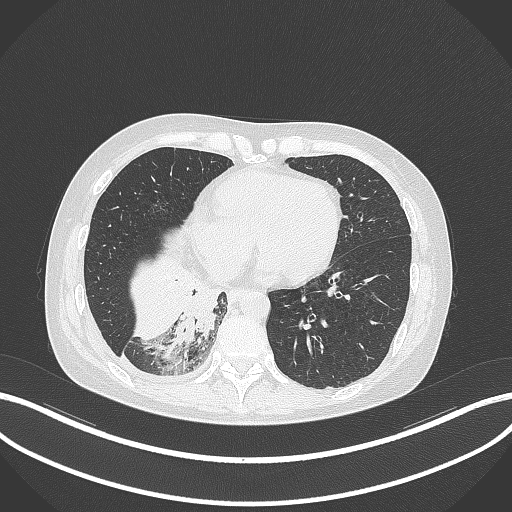
Chest CT, one axial slice. Position 98 of 329 along the scan axis. Reconstruction kernel B70f. Lung window (W 1500 / L -600 HU). 1 mm slice thickness. 512 × 512 image matrix, field of view 400 × 400 mm. Female patient, age 63 years. Case-level facts recorded for this patient, not image findings: clinical TNM (as recorded): T1c N0 M0.
Structures marked on this image (rectangle marked by the reading radiologist):
- lung tumour (recorded histology: adenocarcinoma): bounding box <169,274,223,349> (left, top, right, bottom; pixels)